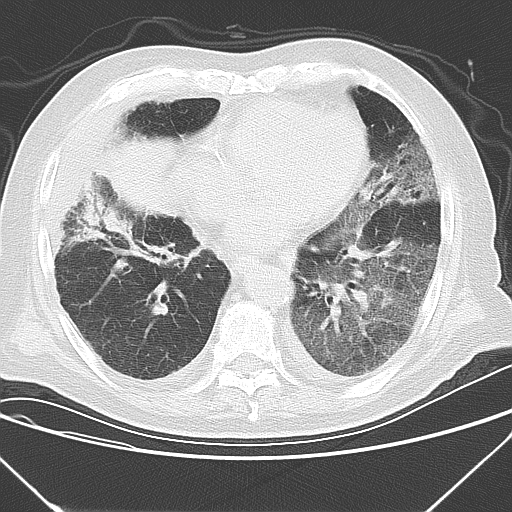
Chest CT, one axial slice. Slice 11 of 43 in the series (ordered by position). 120 kVp. Lung window (W 1500 / L -600 HU). 512 × 512 image matrix, field of view 343 × 343 mm. Patient: male, 85 years. Case-level facts recorded for this patient, not image findings: clinical TNM (as recorded): T4 N3 M2.
Outlined on this slice (bounding box drawn by a radiologist):
- lung tumour (recorded histology: squamous cell carcinoma): bounding box <99,125,178,221> (left, top, right, bottom; pixels)